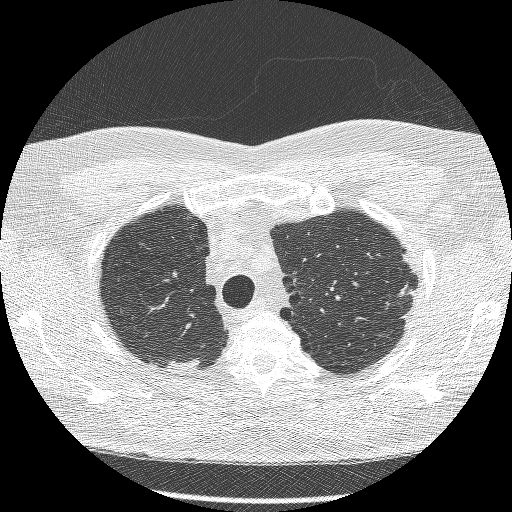
Low-dose screening chest CT, axial slice, second annual screen, lung window (W 1500 / L -600 HU), slice 223 of 269 in the series, 512 × 512 image matrix. Male, age 66 years at enrolment. Current smoker at enrolment.
- Expert-annotated lung lesion, bounding box [x1, y1, x2, y2] px = [382, 258, 431, 315].
- Screening reader's record for this exam (one nodule recorded; not confirmed to be the boxed lesion): non-calcified nodule or mass ≥4 mm, right lower lobe, 40 × 19 mm, spiculated (stellate) margins, soft tissue attenuation, pre-existing on the prior screen: yes; interval growth: no.
- Note: the box lies in the patient's left hemithorax on this image, whereas the reader's record names the right lung; they may be different findings.
- Official screen result: negative screen, minor abnormalities not suspicious for lung cancer.
- Lung cancer was diagnosed 554 days after this screen (after the third annual screen): adenocarcinoma, NOS, left upper lobe, poorly differentiated (G3), stage IB (AJCC 6th edition), 16 mm at pathology.